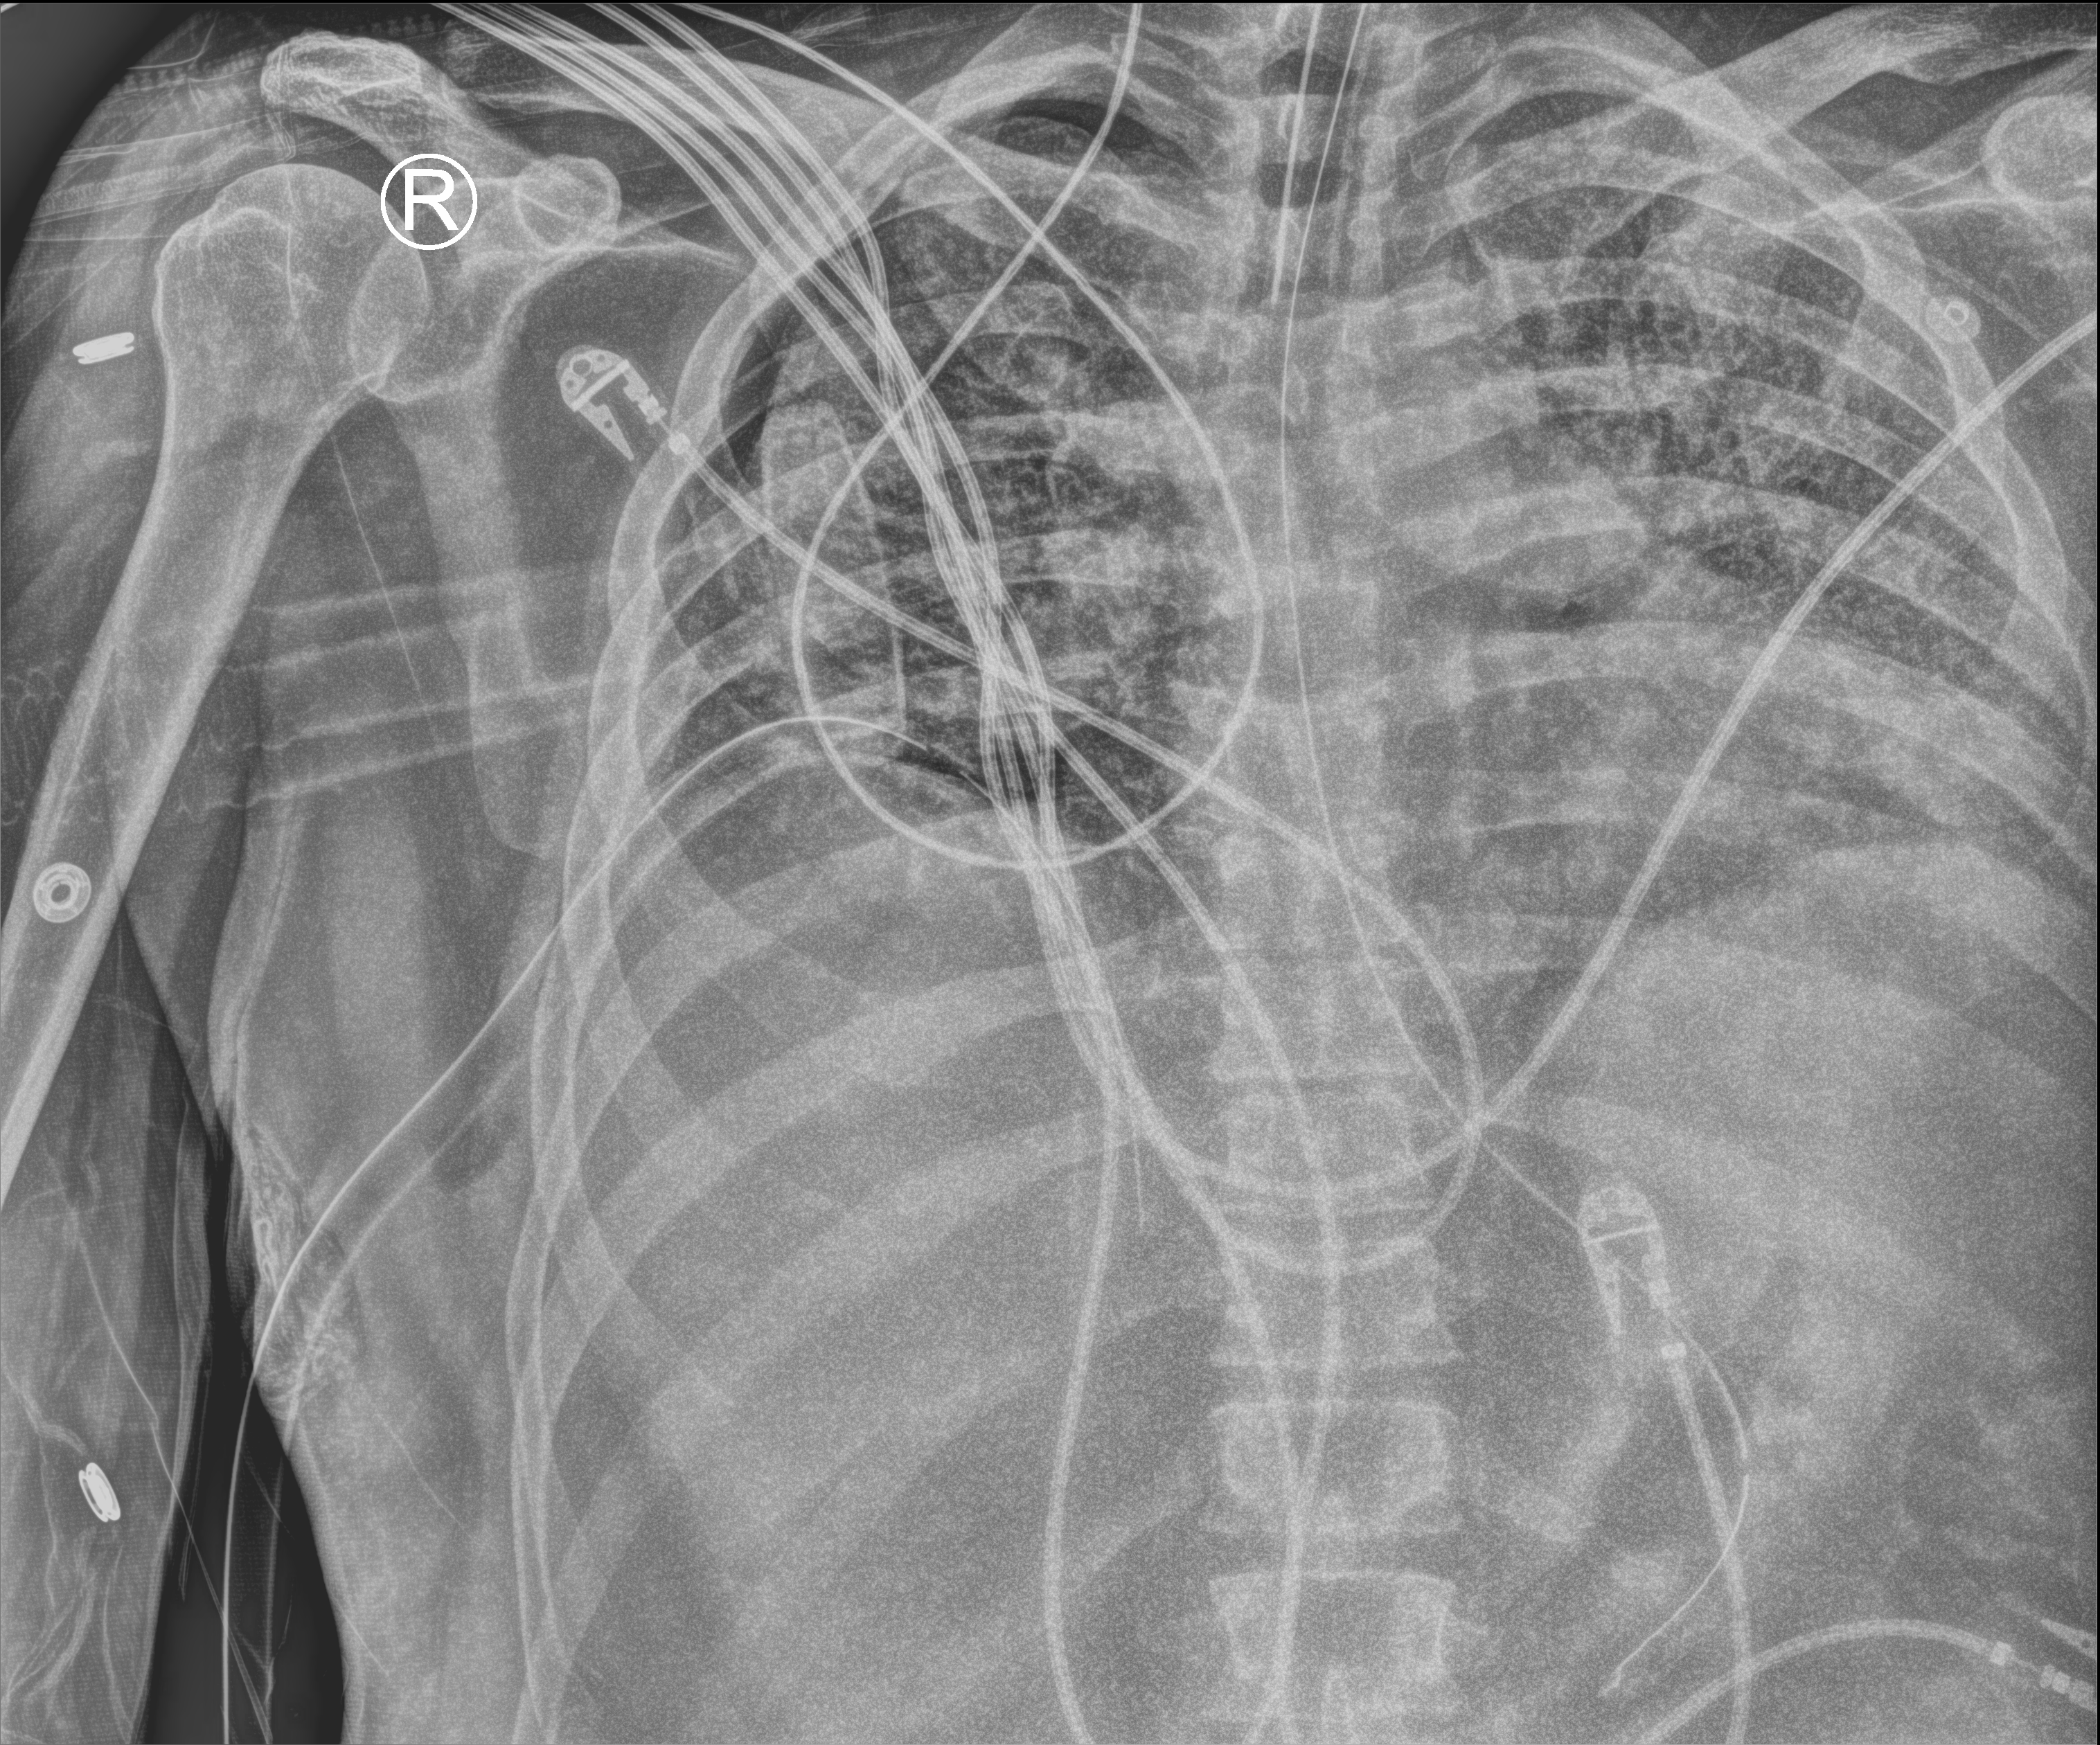
Bedside chest radiograph (computed radiography), anteroposterior (AP) projection. Patient hospitalised with COVID-19; male, aged 18–59 years.
Hospital-stay facts (about this admission, not read from this image; timing relative to this image not recorded): COPD (admission record): no; admitted to intensive care during this hospital stay: yes.